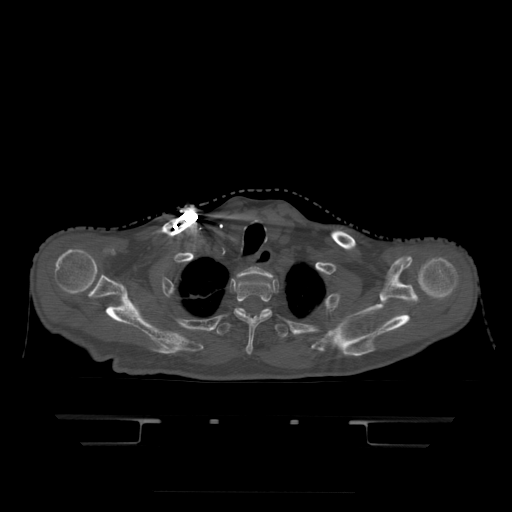
CT including the spine, one axial slice. Position 383 of 522 along the scan axis. Bone window (W 1800 / L 400 HU). 1.25 mm slice thickness. 512 × 512 image matrix. Patient age 68 years. Case-level facts recorded for this patient, not image findings: primary cancer: urothelial.
Outlined on this slice (semi-automatically segmented with operator editing):
- T1 vertebra: bounding box (x1, y1, x2, y2) in pixels: (236, 267, 272, 278)
- T2 vertebra: (234, 279, 274, 356)
- T3 vertebra: (217, 308, 288, 339)